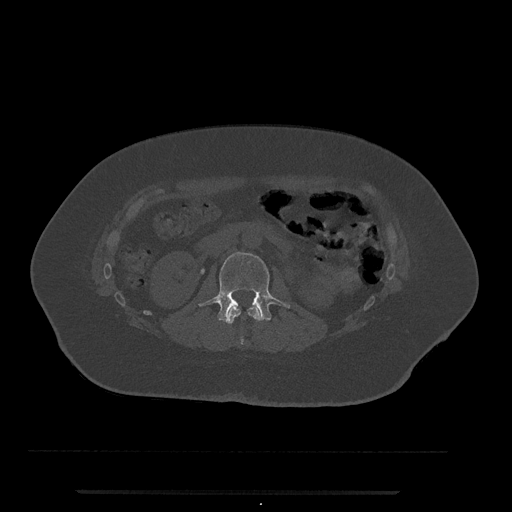
CT including the spine, one axial slice; slice 53 of 797 in the series (ordered by position); reconstruction kernel Br40s/3; 120 kVp; bone window (W 1800 / L 400 HU); 0.5 mm slice thickness; 512 × 512 image matrix, field of view 440 × 440 mm. Female patient, age 51 years. From the clinical record (not read from this slice): primary cancer: neuro.
Outlined on this slice (semi-automatic segmentation, software-assisted and operator-edited):
- L1 vertebra: bounding box <225,306,262,345> (left, top, right, bottom; pixels)
- L2 vertebra: <199,252,290,322>